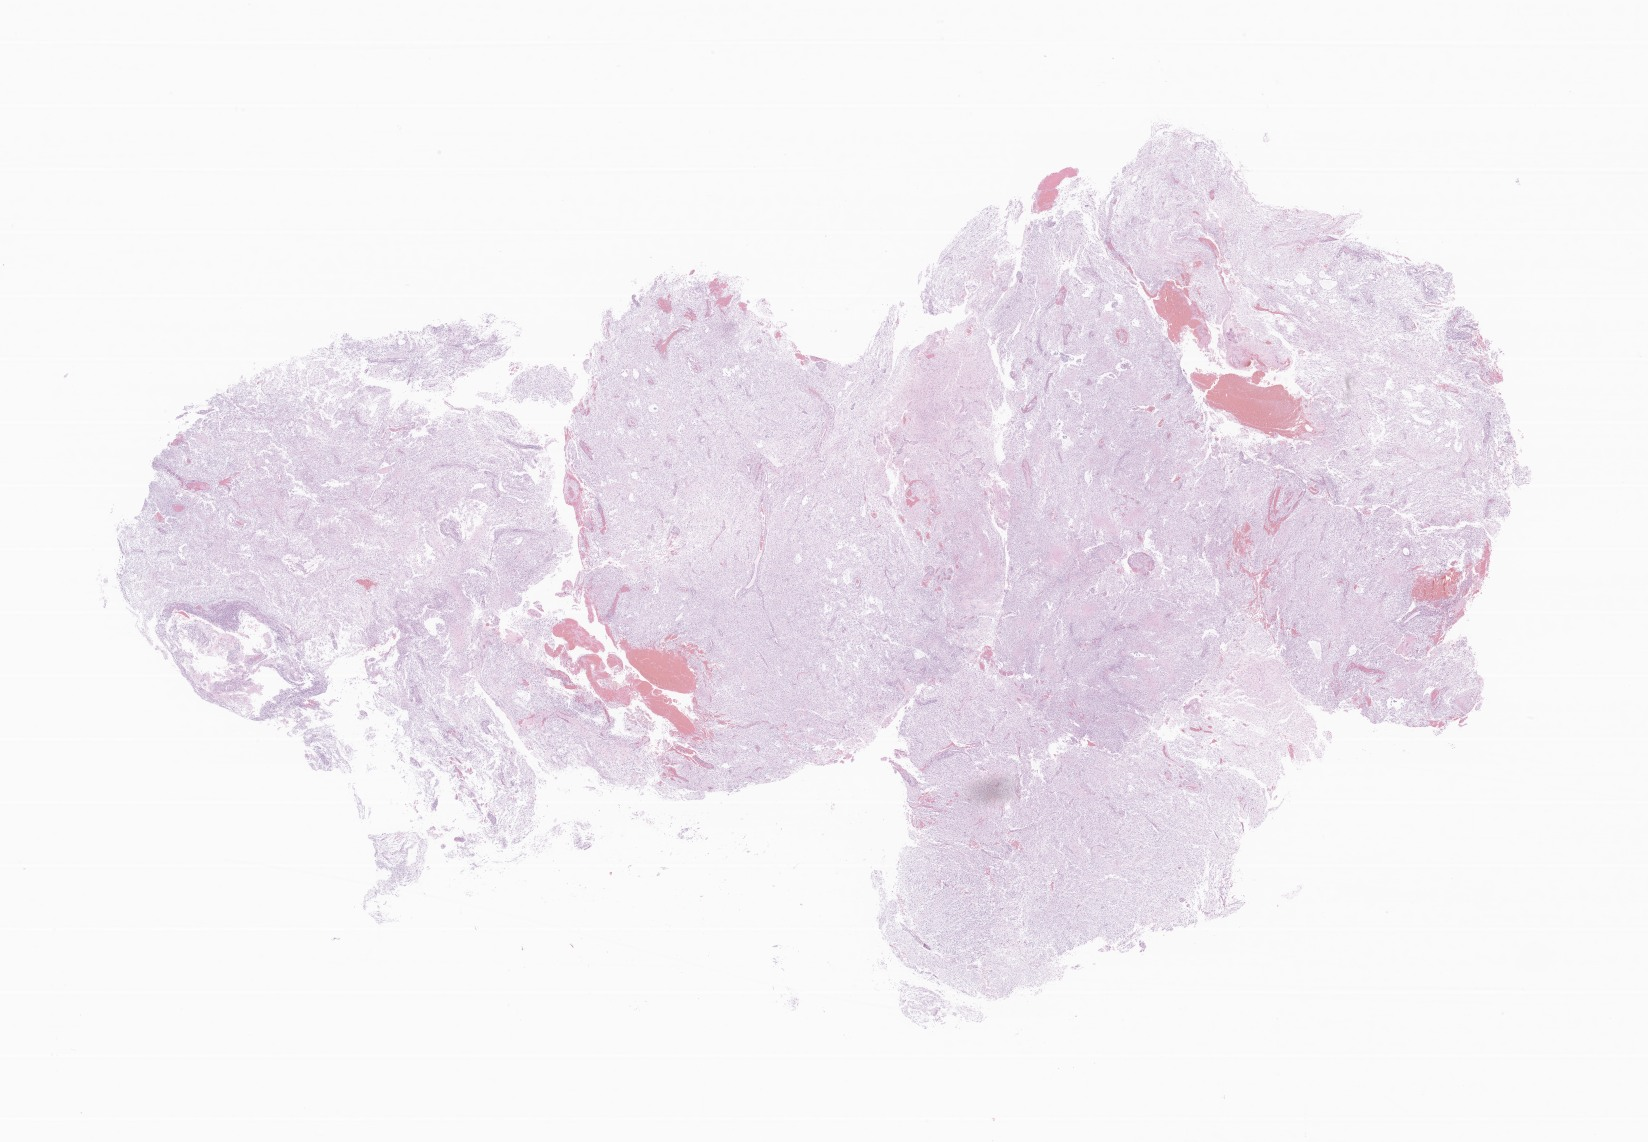
Hematoxylin and eosin (H&E) whole-slide image of tumor tissue from the cerebellum, a low-resolution overview of the entire scanned area, about 27.8 x 19.3 mm; formalin-fixed paraffin-embedded section. Patient: male, age 83 months (6 years 11 months).
- diagnosis: Pilocytic astrocytoma